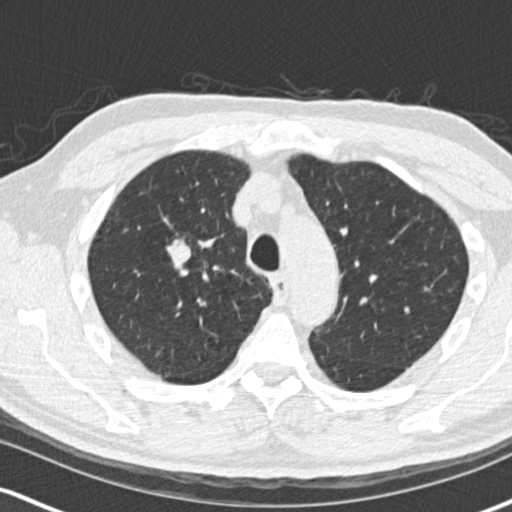
Low-dose screening chest CT, one axial slice; reconstruction kernel B30f; lung window (W 1500 / L -600 HU); 2 mm slice thickness; 512 × 512 image matrix.
Annotated regions visible in this slice (outlined manually by an expert reader):
- lesion 1 (tumor, upper lobe of right lung): box from (x=166, y=241) to (x=191, y=267) px